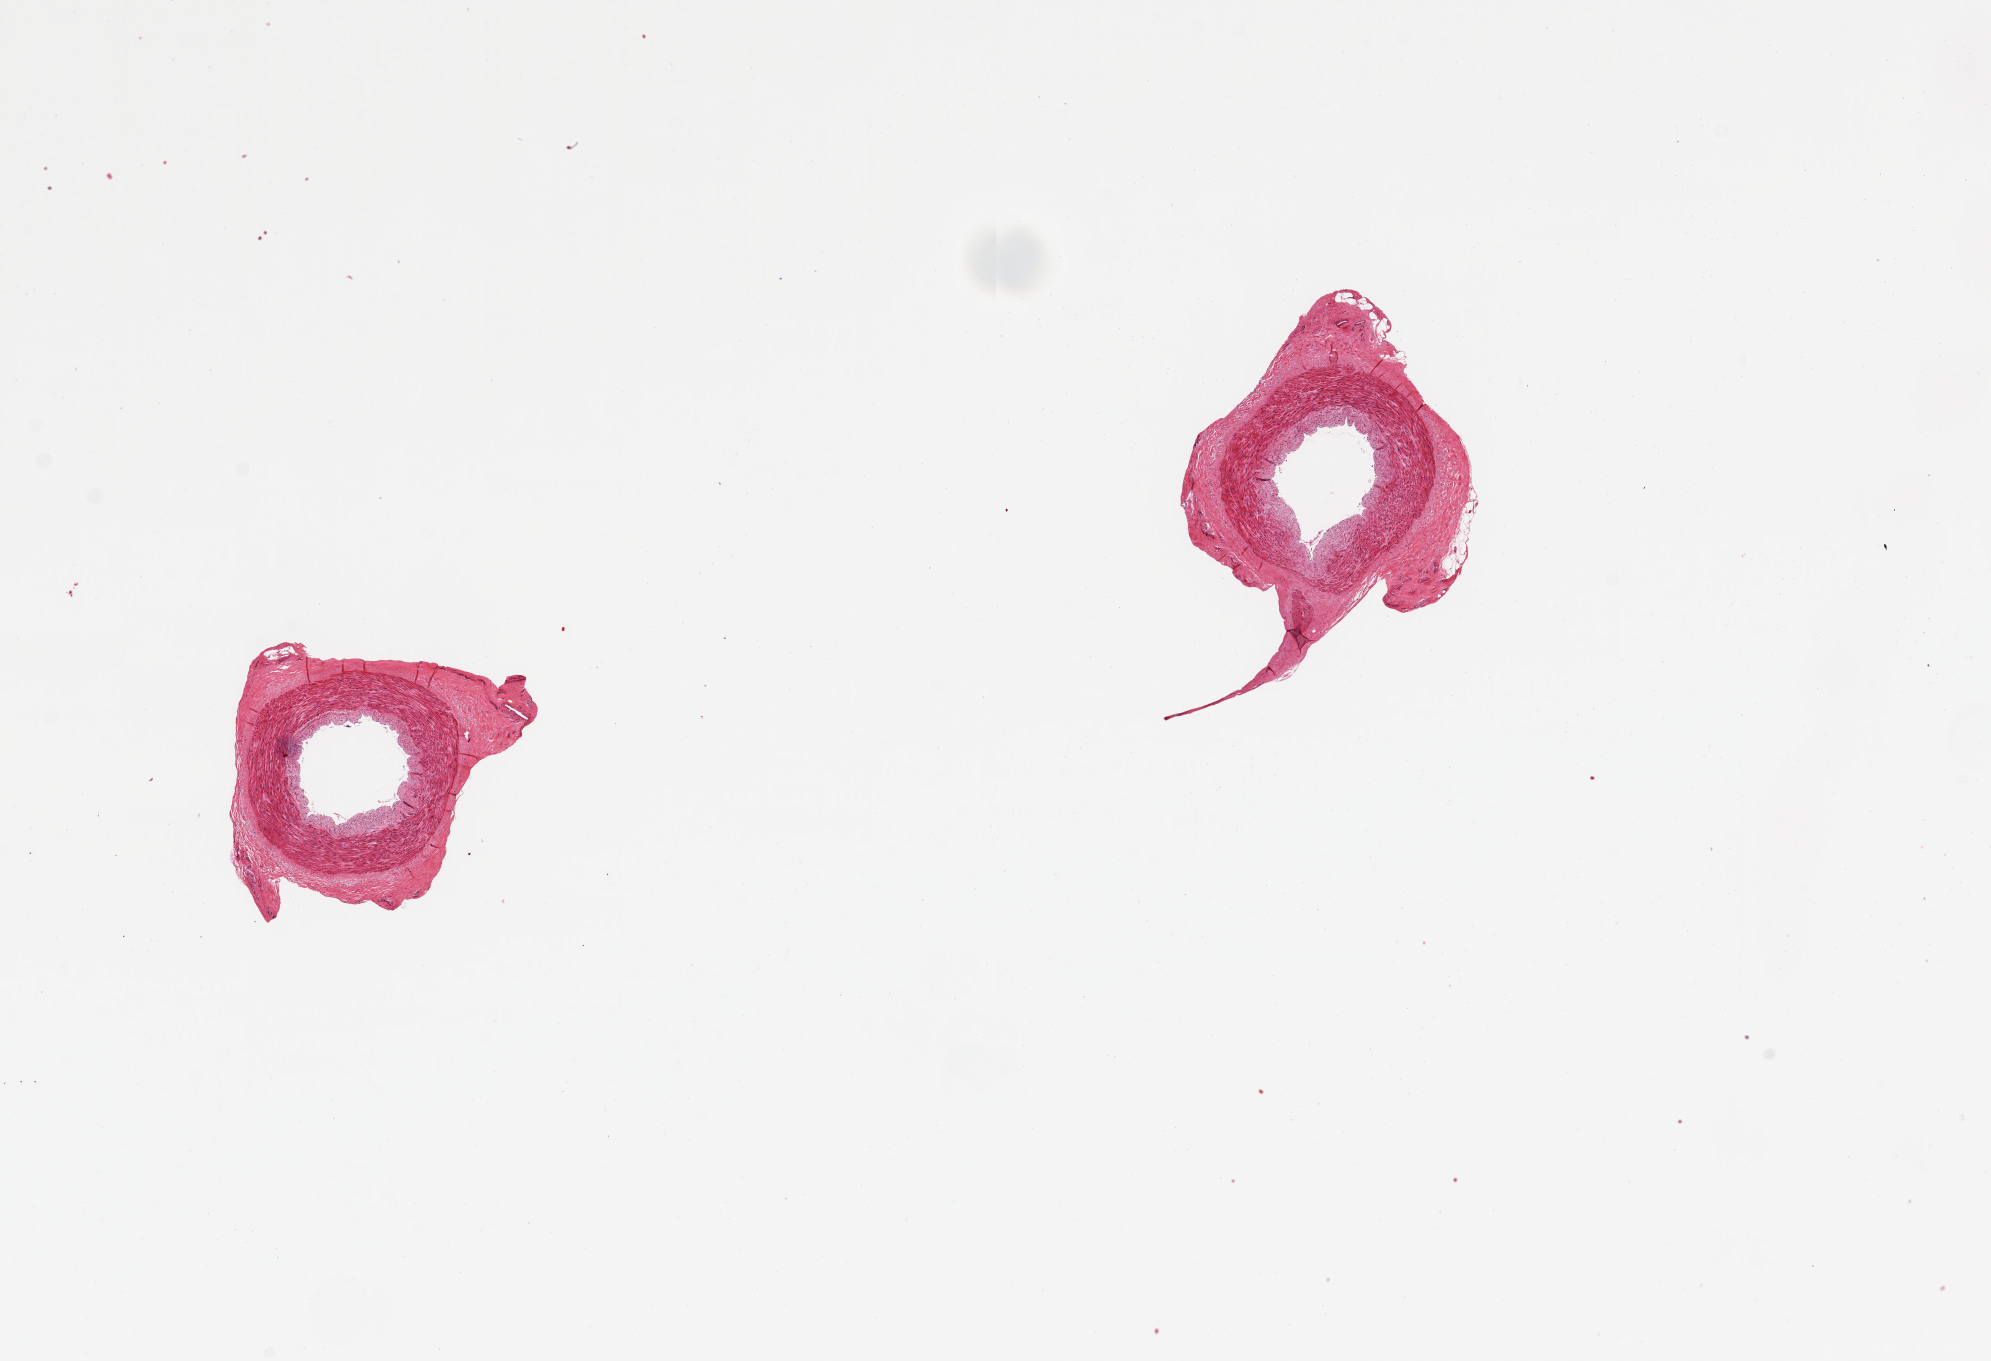
H&E whole-slide image, low-resolution overview of the scanned area, about 15.8 x 10.8 mm, PAXgene-fixed paraffin-embedded (PFPE) section, sampled site (target tissue): tibial artery, tissue donor sample. Donor sex: male.
Reviewer comment on this tissue sample: 2 pieces, ~1.5mm d.; discontinuous adherent fibrous tissue up to ~0.5mm.